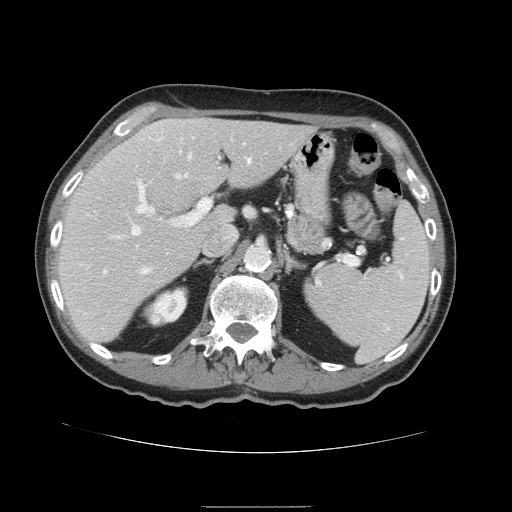
Contrast-enhanced abdominal CT, one axial slice. Slice 96 of 168 in the series (ordered by position). Intravenous contrast given. Soft-tissue window (W 400 / L 40 HU). 2.5 mm slice thickness. 512 × 512 image matrix, field of view 386 × 386 mm. Male patient, age 74 years. From the clinical record (not read from this slice): diagnosis: colorectal cancer liver metastases, imaged before liver resection; multiple liver metastases: no; largest metastasis: 14.5 cm; disease in both lobes: yes.
Outlined on this slice (outlined manually by an expert reader):
- hepatic veins: box from (x=131, y=155) to (x=251, y=272) px
- liver: (x=58, y=119)–(x=316, y=344)
- planned liver remnant (the part of the liver to remain after resection): (x=58, y=119)–(x=316, y=344)
- portal vein (with intrahepatic branches): (x=93, y=183)–(x=211, y=272)